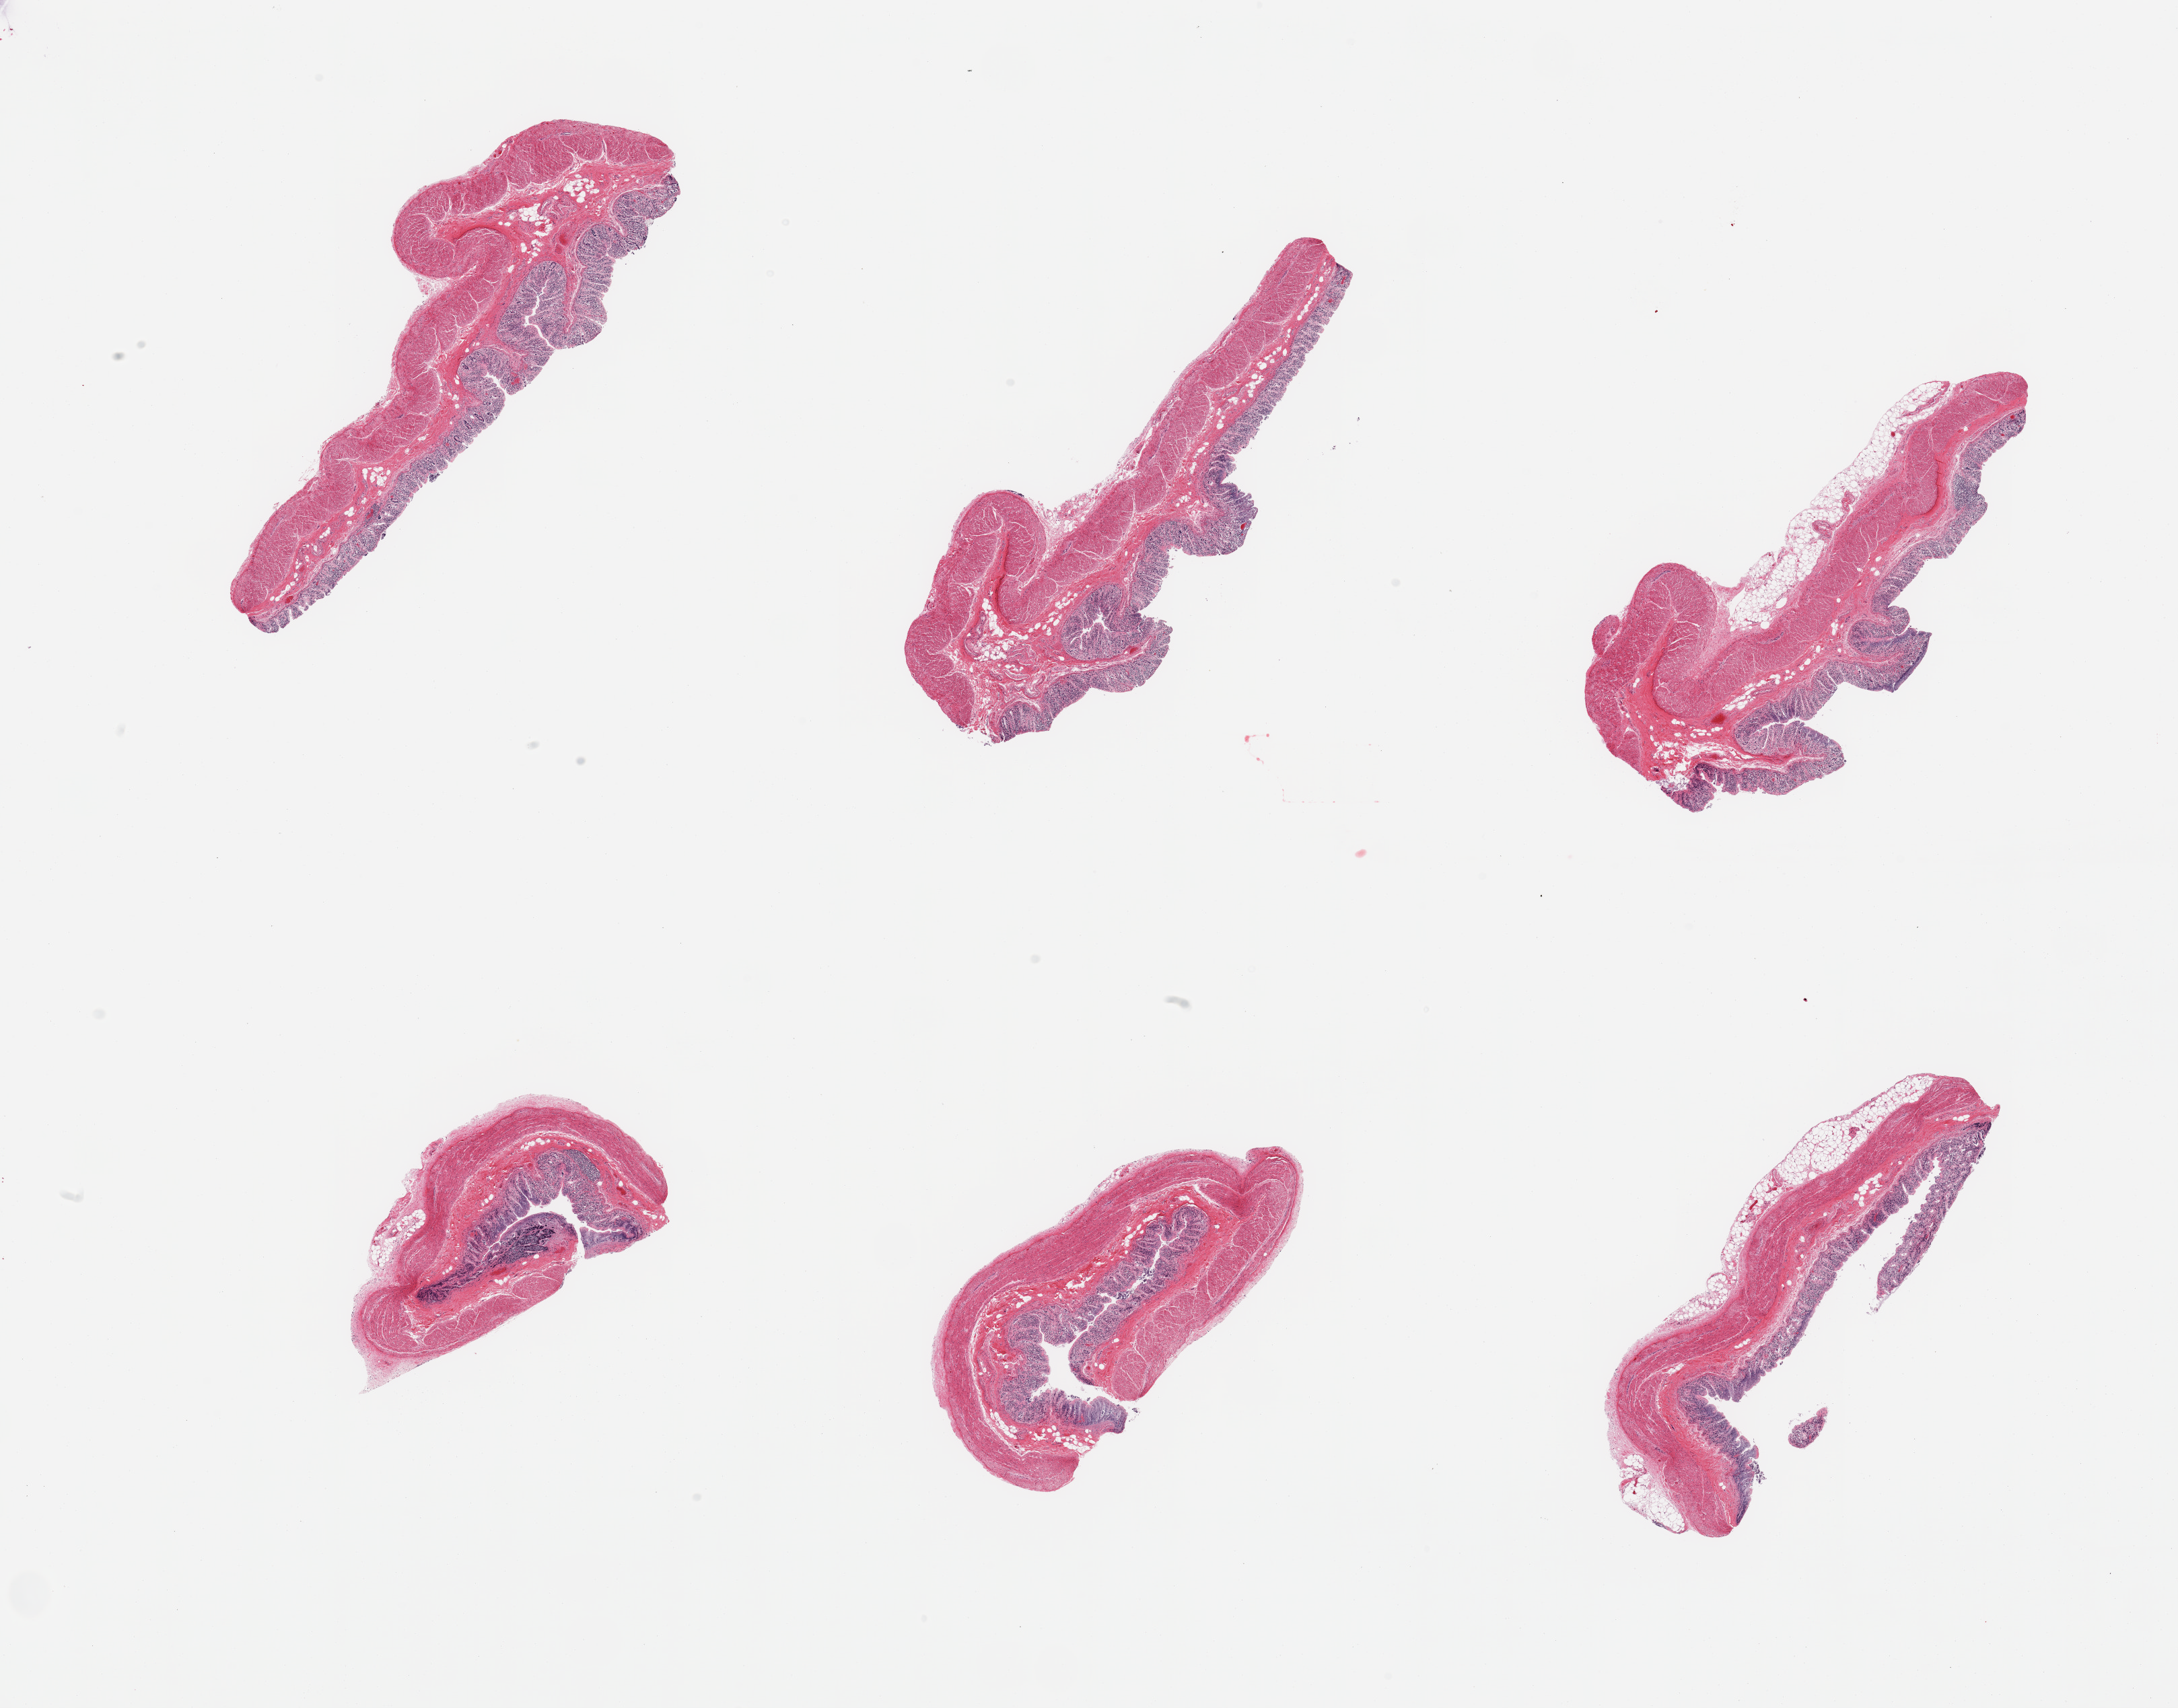
Haematoxylin and eosin whole-slide image, brightfield, a low-resolution overview of the entire scanned area, about 25.6 x 20.1 mm (acquisition: 20x scan); PAXgene-fixed, paraffin-embedded tissue; sampled site (target tissue): transverse colon; tissue donor sample.
Reviewer comment on this tissue sample: 6 pieces; mucosal glands totally autolyzed [3]; muscle intact [2].